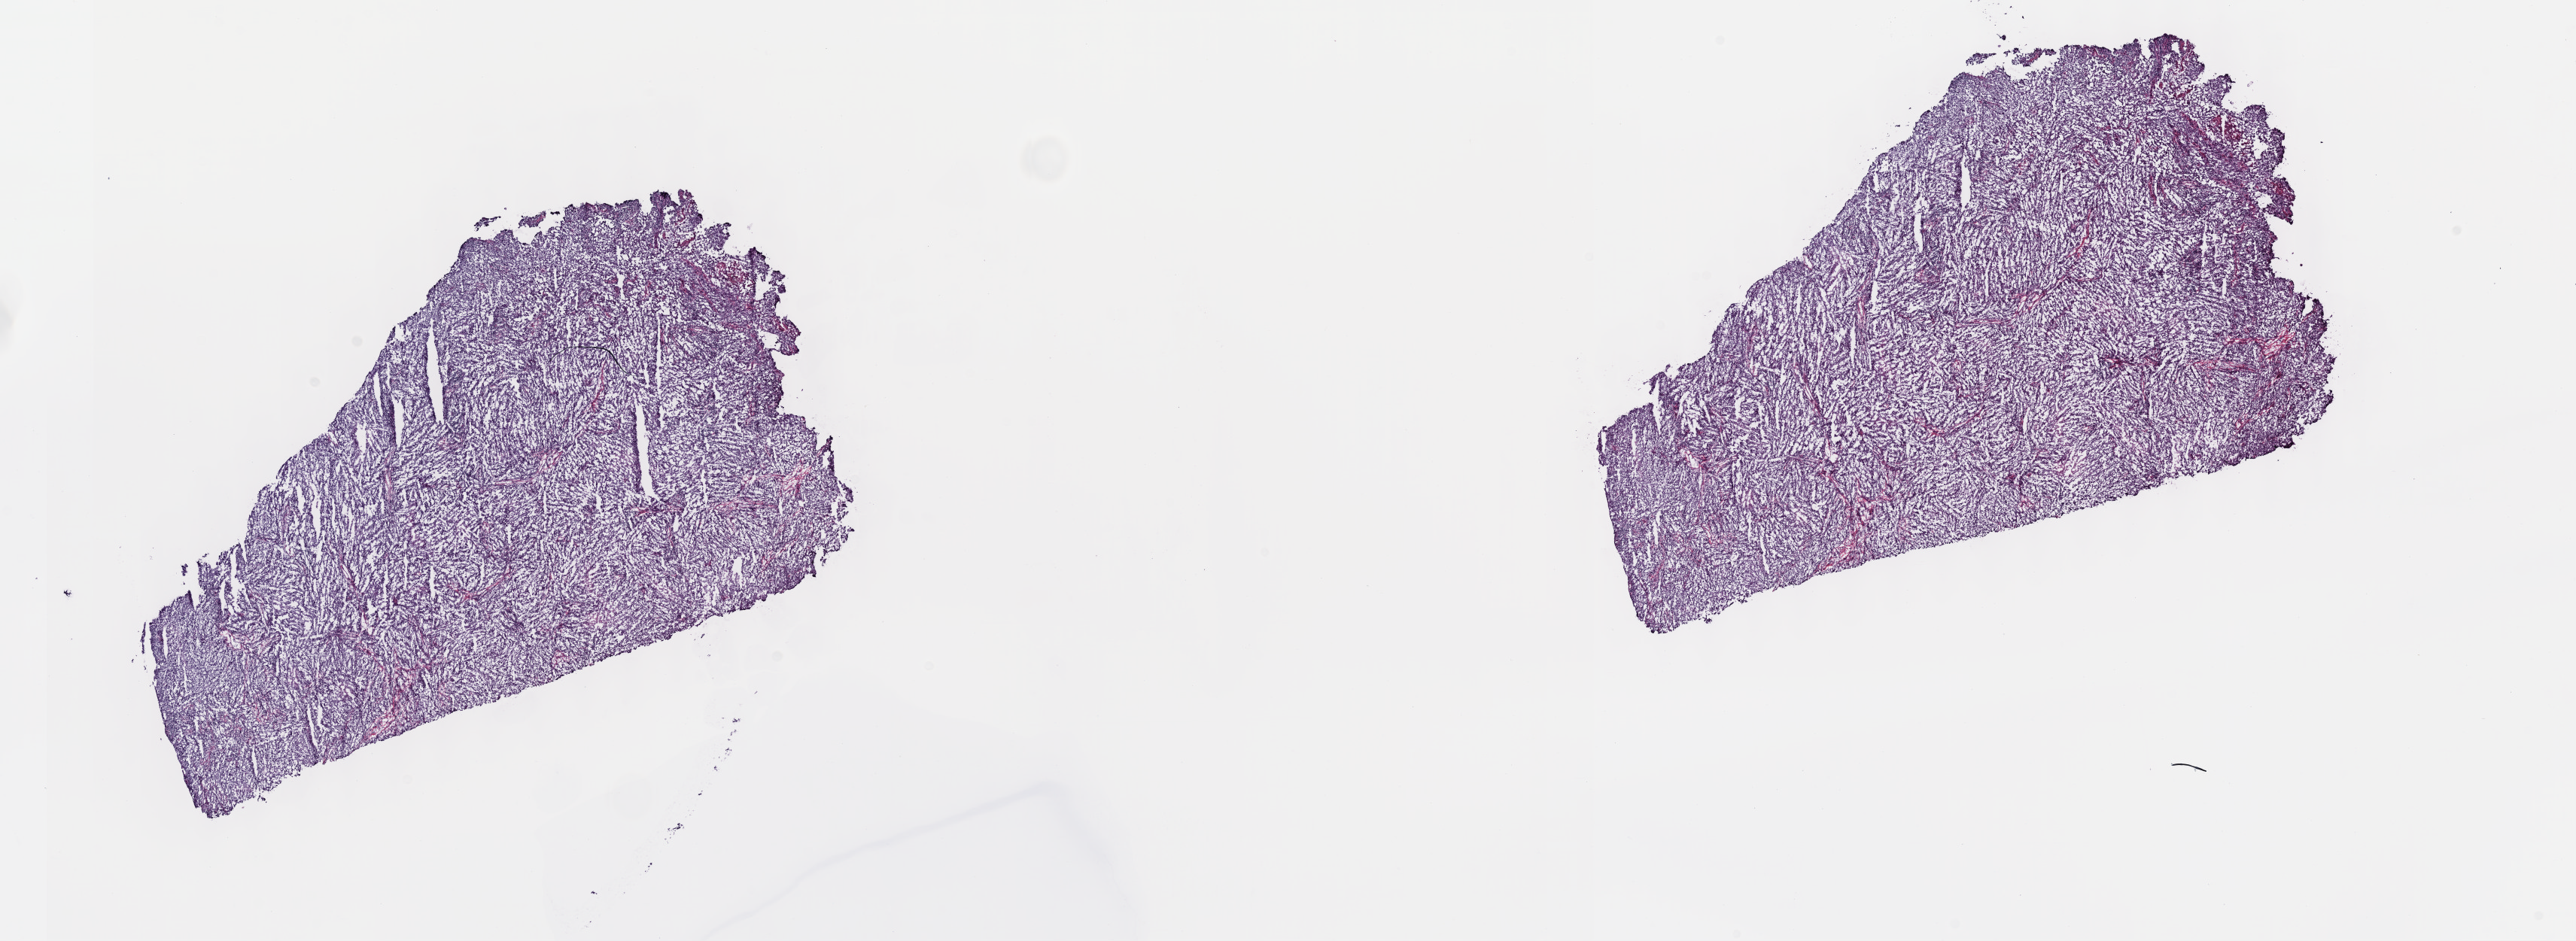
Digitized H&E tissue section (whole slide), shown as a low-resolution overview of the whole scanned area (about 27.7 x 10.1 mm, acquisition: 40x scan), frozen section from the top of the tissue portion, sample: primary tumour, skin. Male, age 85 years at initial diagnosis. Composition of this section per pathologist review: tumour cells 100%, tumour nuclei 80%.
Pathologic diagnosis: Nodular melanoma.